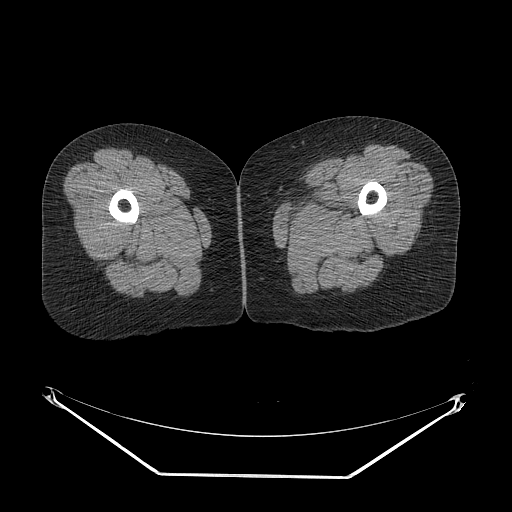
CT of an extremity soft-tissue mass (from a PET/CT study), one axial slice; slice 3 of 267 in the series (ordered by position); 140 kVp; soft-tissue window (W 400 / L 40 HU); 3.75 mm slice thickness; 512 × 512 image matrix, field of view 500 × 500 mm. Female patient. Case-level facts recorded for this patient, not image findings: histological type: myxofibrosarcoma; grade: intermediate; site of the primary tumour: left thigh.
Structures marked on this image (expert contour drawn on MRI and transferred to this co-registered scan by the dataset authors):
- gross tumour volume including surrounding oedema: bounding box <290,206,348,232> (left, top, right, bottom; pixels)